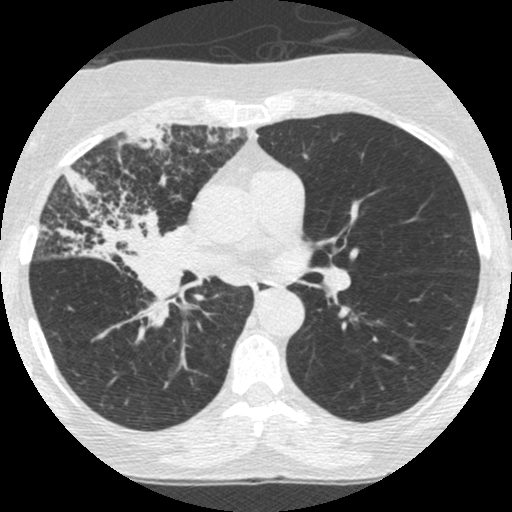
Low-dose screening chest CT, one axial slice; slice 144 of 253 in the series (ordered by position); reconstruction kernel STANDARD; lung window (W 1500 / L -600 HU); 1.25 mm slice thickness; 512 × 512 image matrix, field of view 294 × 294 mm.
Annotated regions visible in this slice (outlined manually by an expert reader):
- lesion 2 (tumor, hilum of right lung): bounding box [x1, y1, x2, y2] px = [39, 167, 187, 329]
- lesion 3 (tumor, upper lobe of right lung): [123, 124, 174, 165]
- lesion 4 (tumor, upper lobe of right lung): [205, 125, 242, 149]